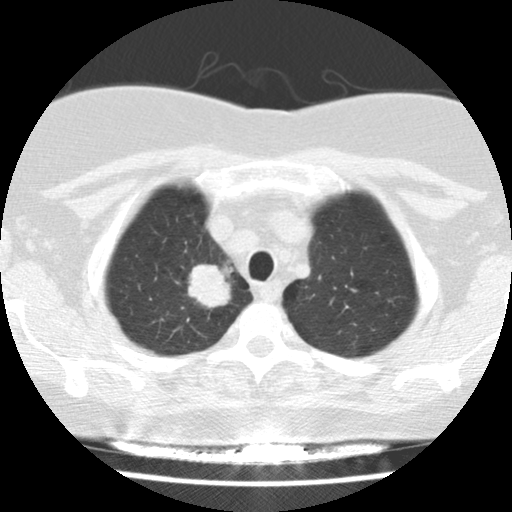
Axial slice from a low-dose chest CT screening exam. Baseline screening round. Lung window (W 1500 / L -600 HU). Slice 21 of 148 in the series. 512 × 512 image matrix. Female participant, aged 58 years at enrolment. Former smoker at enrolment.
Expert reader's lesion annotation, bounding box (x1, y1, x2, y2) in pixels: (169, 246, 247, 324). The exam's reader record, not a measurement of the box and not confirmed to be the same lesion: non-calcified nodule or mass ≥4 mm, right upper lobe, 28 × 24 mm, spiculated (stellate) margins, soft tissue attenuation. Participant outcome: lung cancer diagnosed 40 days after this screen — adenocarcinoma, NOS, right upper lobe, poorly differentiated (G3), stage IB (AJCC 6th edition), 29 mm at pathology.